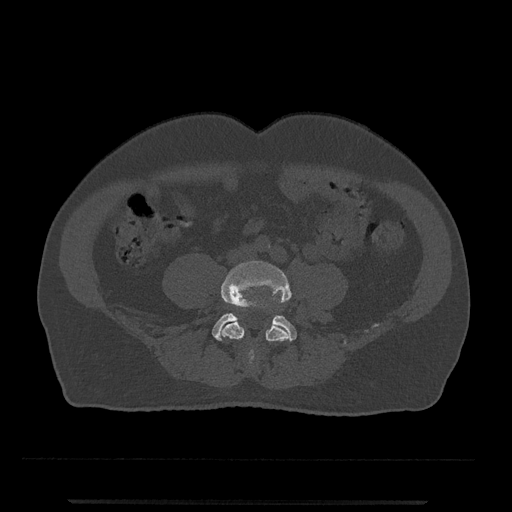
CT including the spine, one axial slice; position 107 of 797 along the scan axis; 120 kVp; bone window (W 1800 / L 400 HU); 0.5 mm slice thickness; 512 × 512 image matrix, field of view 419 × 419 mm. Patient: male, 63 years. Case-level facts recorded for this patient, not image findings: primary cancer: prostate.
Annotated regions visible in this slice (semi-automatic segmentation, software-assisted and operator-edited):
- L4 vertebra: bounding box [x1, y1, x2, y2] px = [220, 261, 292, 365]
- L5 vertebra: [212, 313, 297, 341]